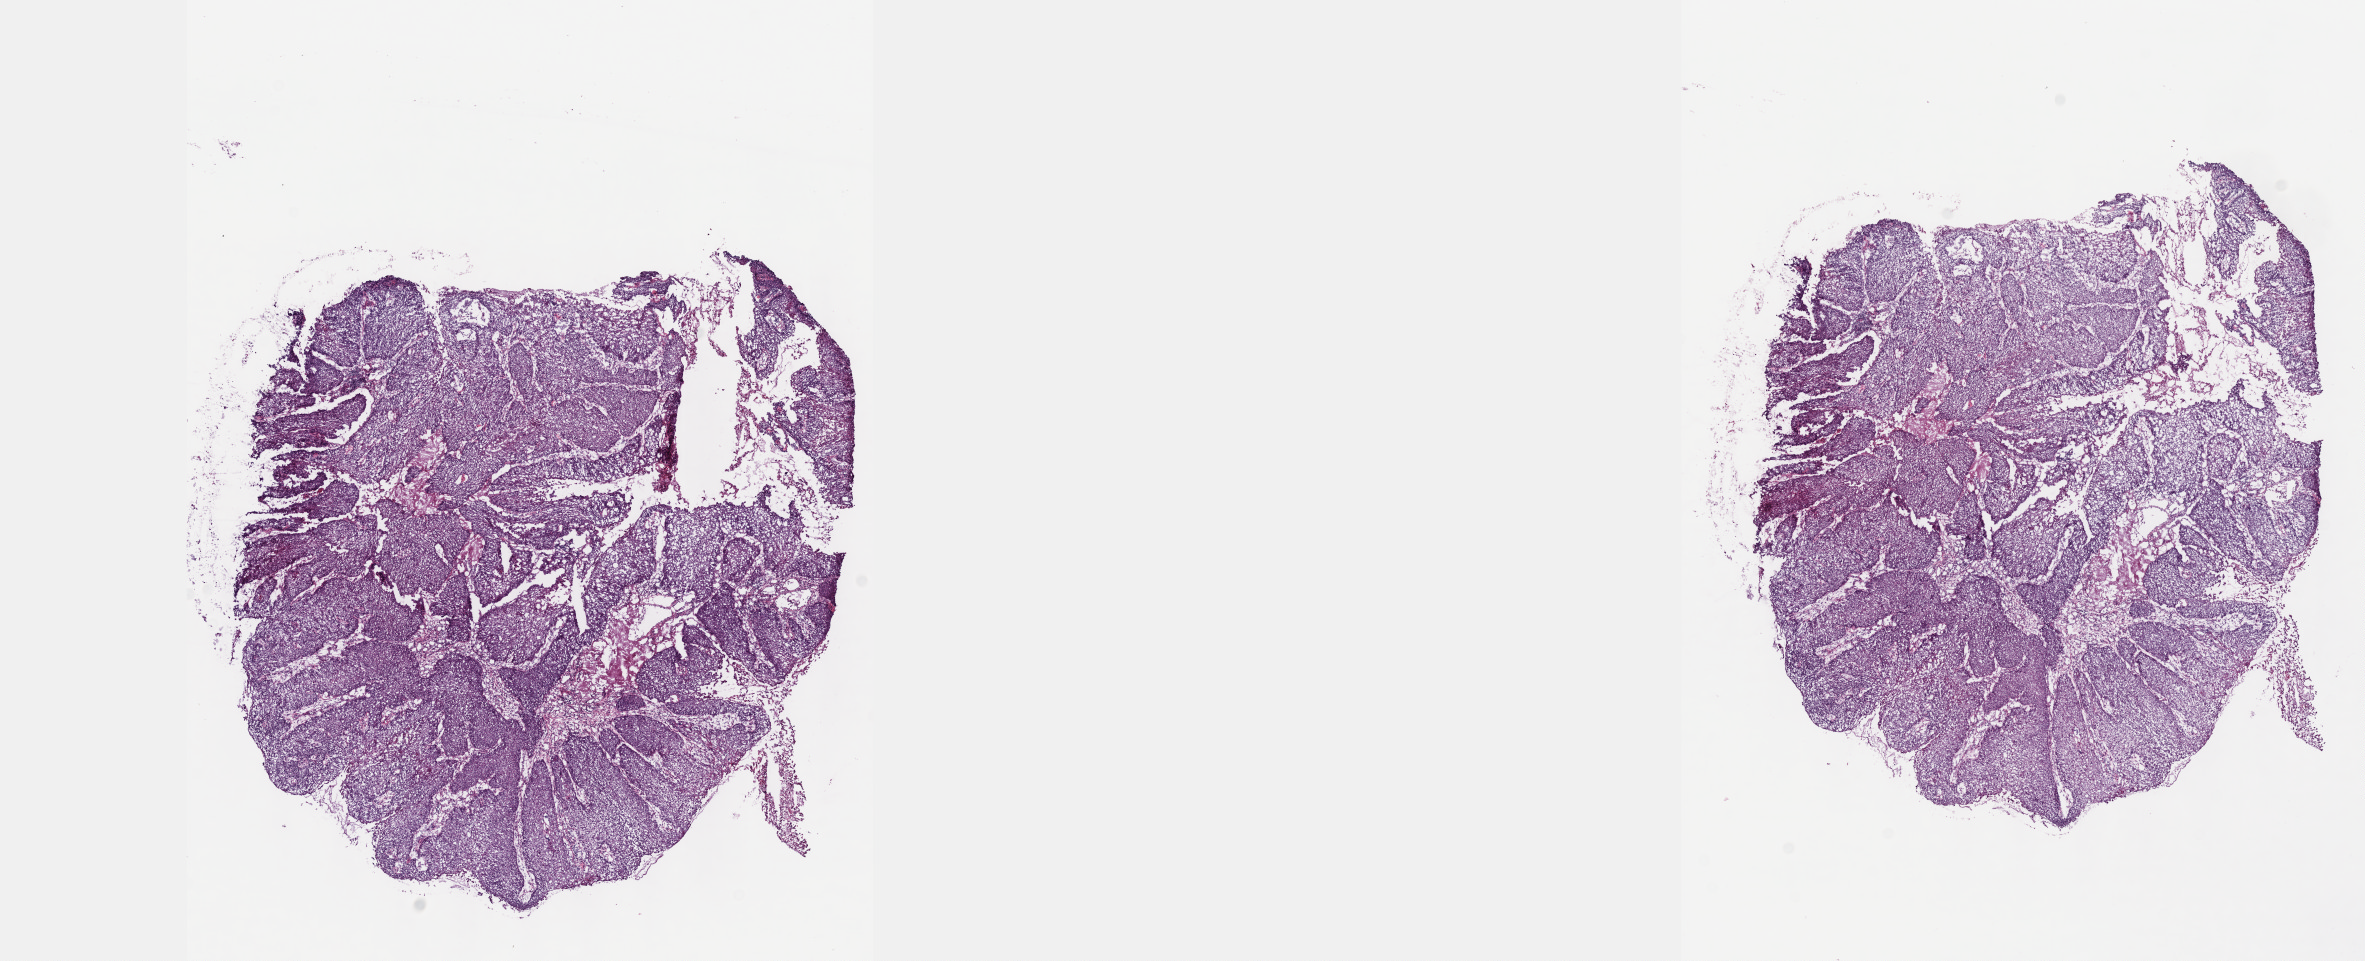
Whole-slide histology image, Hematoxylin and eosin (H&E) stained — a low-resolution overview of the entire scanned area, about 19.1 x 7.8 mm (from a 40x scan); frozen section; sample: primary tumour, cervix. Patient: female, age at initial diagnosis 74 years. Slide review estimates, as recorded: tumour cells 70%, tumour nuclei 70%.
Histologic diagnosis: Squamous cell carcinoma, NOS (cervix uteri).